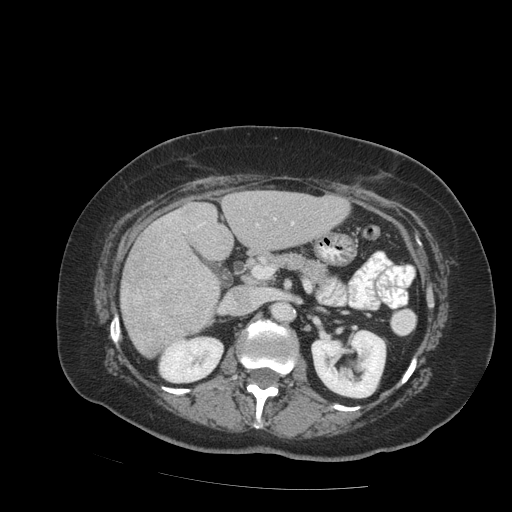
Contrast-enhanced abdominal CT (liver protocol), one axial slice. Slice 40 of 99 in the series (ordered by position). Reconstruction kernel STANDARD. 140 kVp. Soft-tissue window (W 400 / L 40 HU). 2.5 mm slice thickness. 512 × 512 image matrix. From the clinical record (not read from this slice): diagnosis: hepatocellular carcinoma (patient treated with transarterial chemoembolisation; whether this scan precedes or follows treatment is not stated here); TNM stage (as recorded): Stage-IVB; Child-Pugh class: A; tumour differentiation: moderately differentiated.
Annotated regions visible in this slice (semi-automatically segmented with operator editing):
- liver parenchyma outside the tumour (the mass and vessels are separate outlines, so this box may not span the whole liver): bounding box [x1, y1, x2, y2] px = [120, 190, 349, 356]
- mass: [122, 239, 216, 353]
- liver vessels: [199, 218, 294, 226]